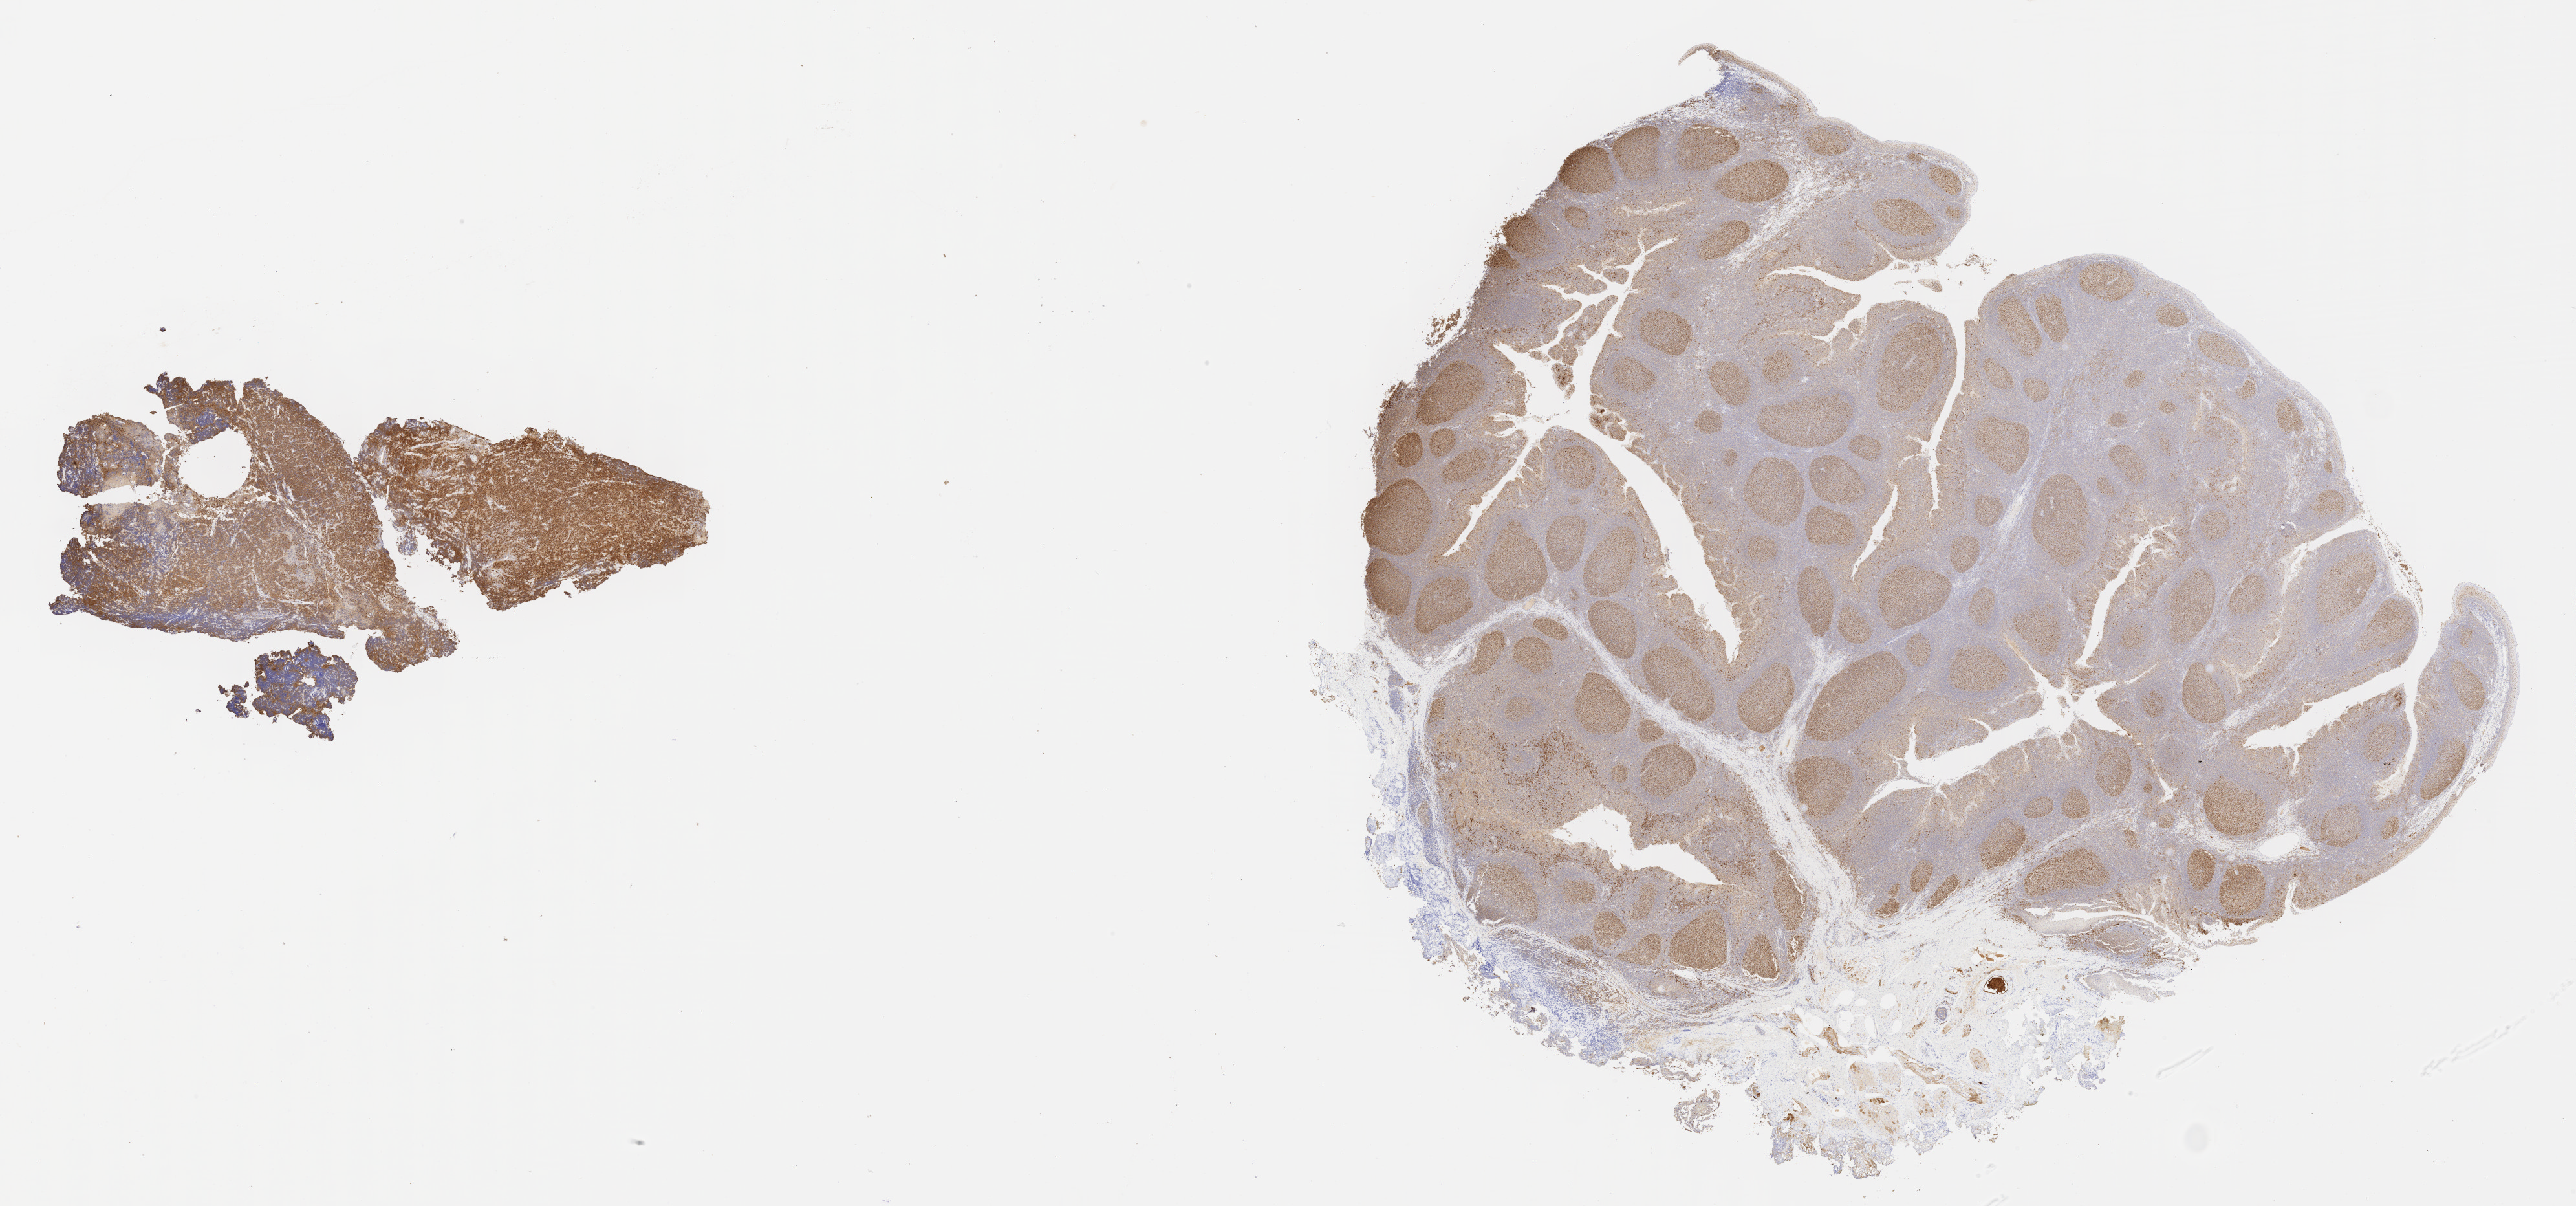
IHC for BCL6, whole-slide image, shown as a low-resolution overview of the whole scanned area (about 32.2 x 15.1 mm), tumor tissue, site: mandible. Male patient, age 25 years.
Diagnosis: Diffuse large B-cell lymphoma, NOS.